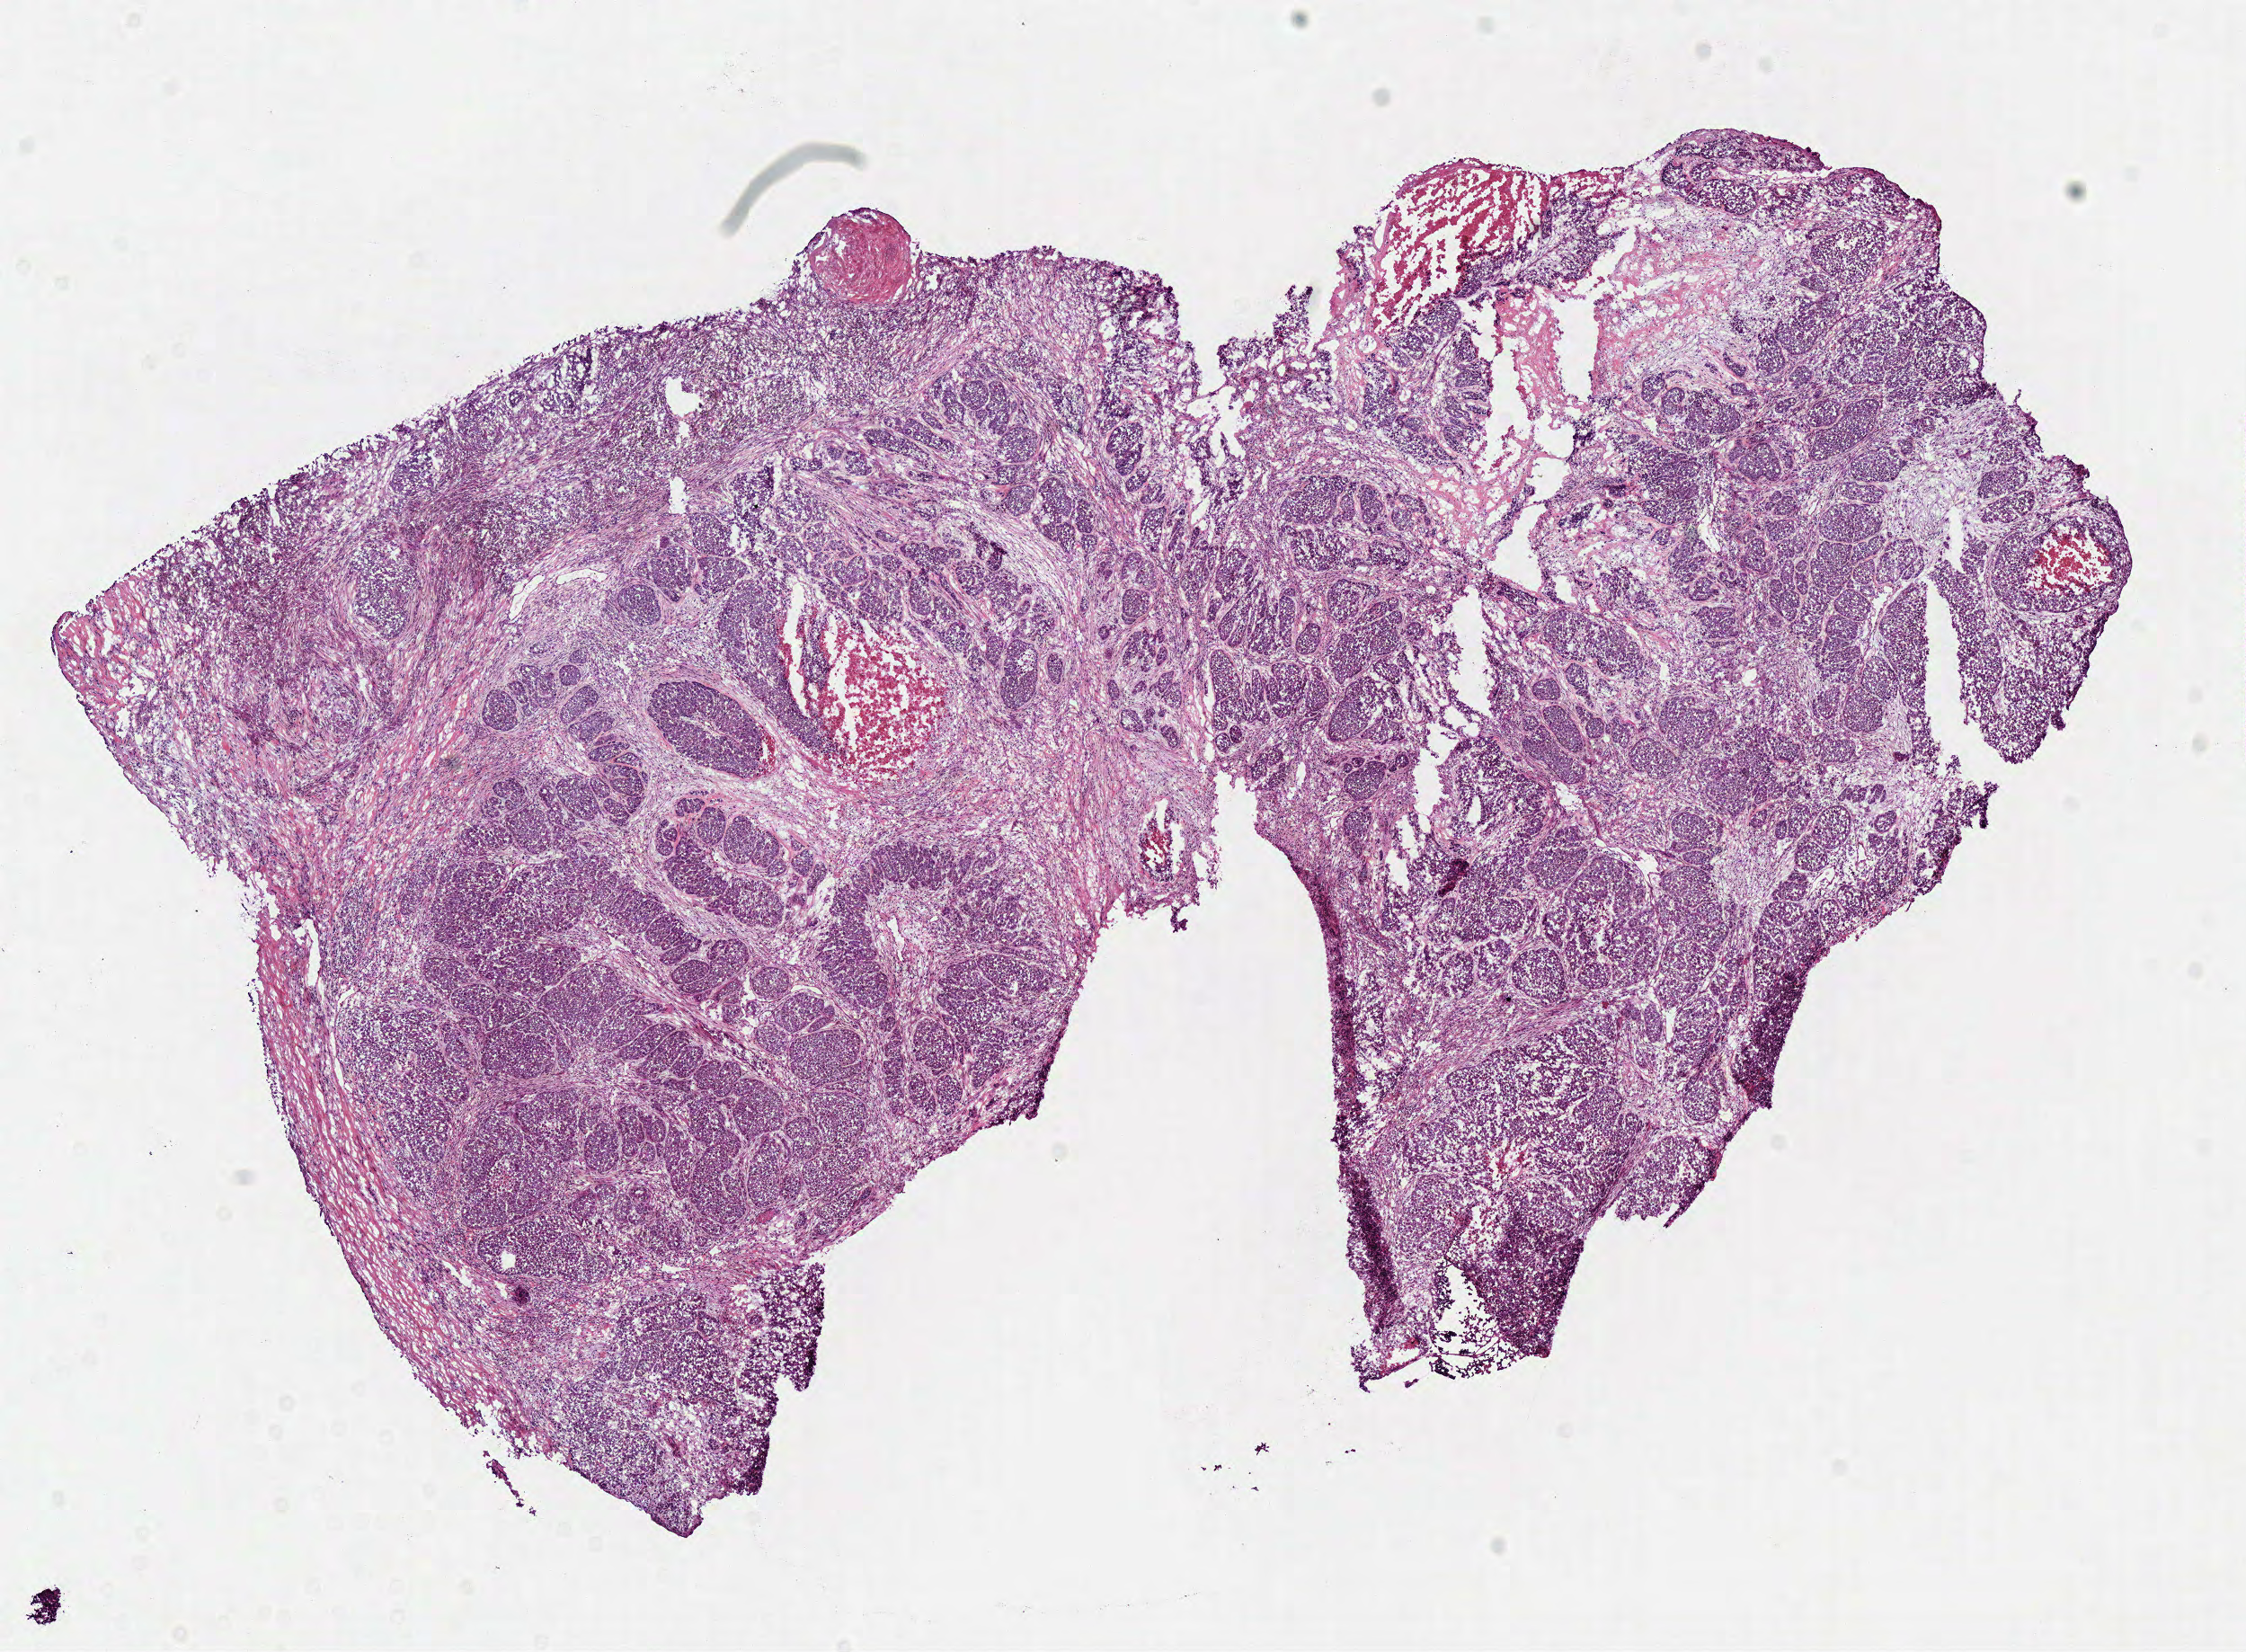
H&E-stained whole-slide image, low-resolution overview of the scanned area, about 9.8 x 7.2 mm (slide scanned at 40x); frozen section from the top of the tissue portion; primary tumour sample from the lung. Patient: male, age at initial diagnosis 58 years. Pathologist review of this section (percent, as recorded): tumour cells 70%, tumour nuclei 80%, normal cells 0%, stromal cells 20%, necrosis 10%. Inflammatory infiltration, as recorded: lymphocyte infiltration 10%, monocyte infiltration 0%, neutrophil infiltration 0%.
Histologic diagnosis: Adenocarcinoma, NOS (upper lobe, lung).